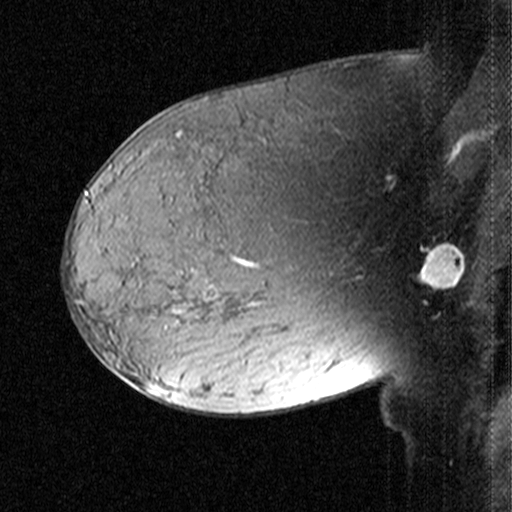
Breast MRI (dynamic contrast-enhanced), one sagittal slice. Slice 26 of 44 in the series (ordered by position). Dynamic contrast-enhanced study with each time point stored as its own series, time point 2 of 3 at this slice position (early post-contrast, ordered by acquisition time). 1.5 T. TE 4.5 ms, TR 11 ms. 3 mm slice thickness. 512 × 512 image matrix, field of view 200 × 200 mm. Female patient, age 38 years. From the clinical record (not read from this slice): setting: breast cancer imaged before/during neoadjuvant chemotherapy; receptor status: HR-positive, HER2-negative.
Structures marked on this image (semi-automatic segmentation, software-assisted and operator-edited):
- analysis volume of interest (the breast-tissue region the enhancement analysis was run in; not a lesion): box from (x=170, y=232) to (x=259, y=331) px
- tumour enhancement mask (voxels above the 90 % enhancement threshold inside the analysis volume of interest): (x=235, y=258)–(x=239, y=261)